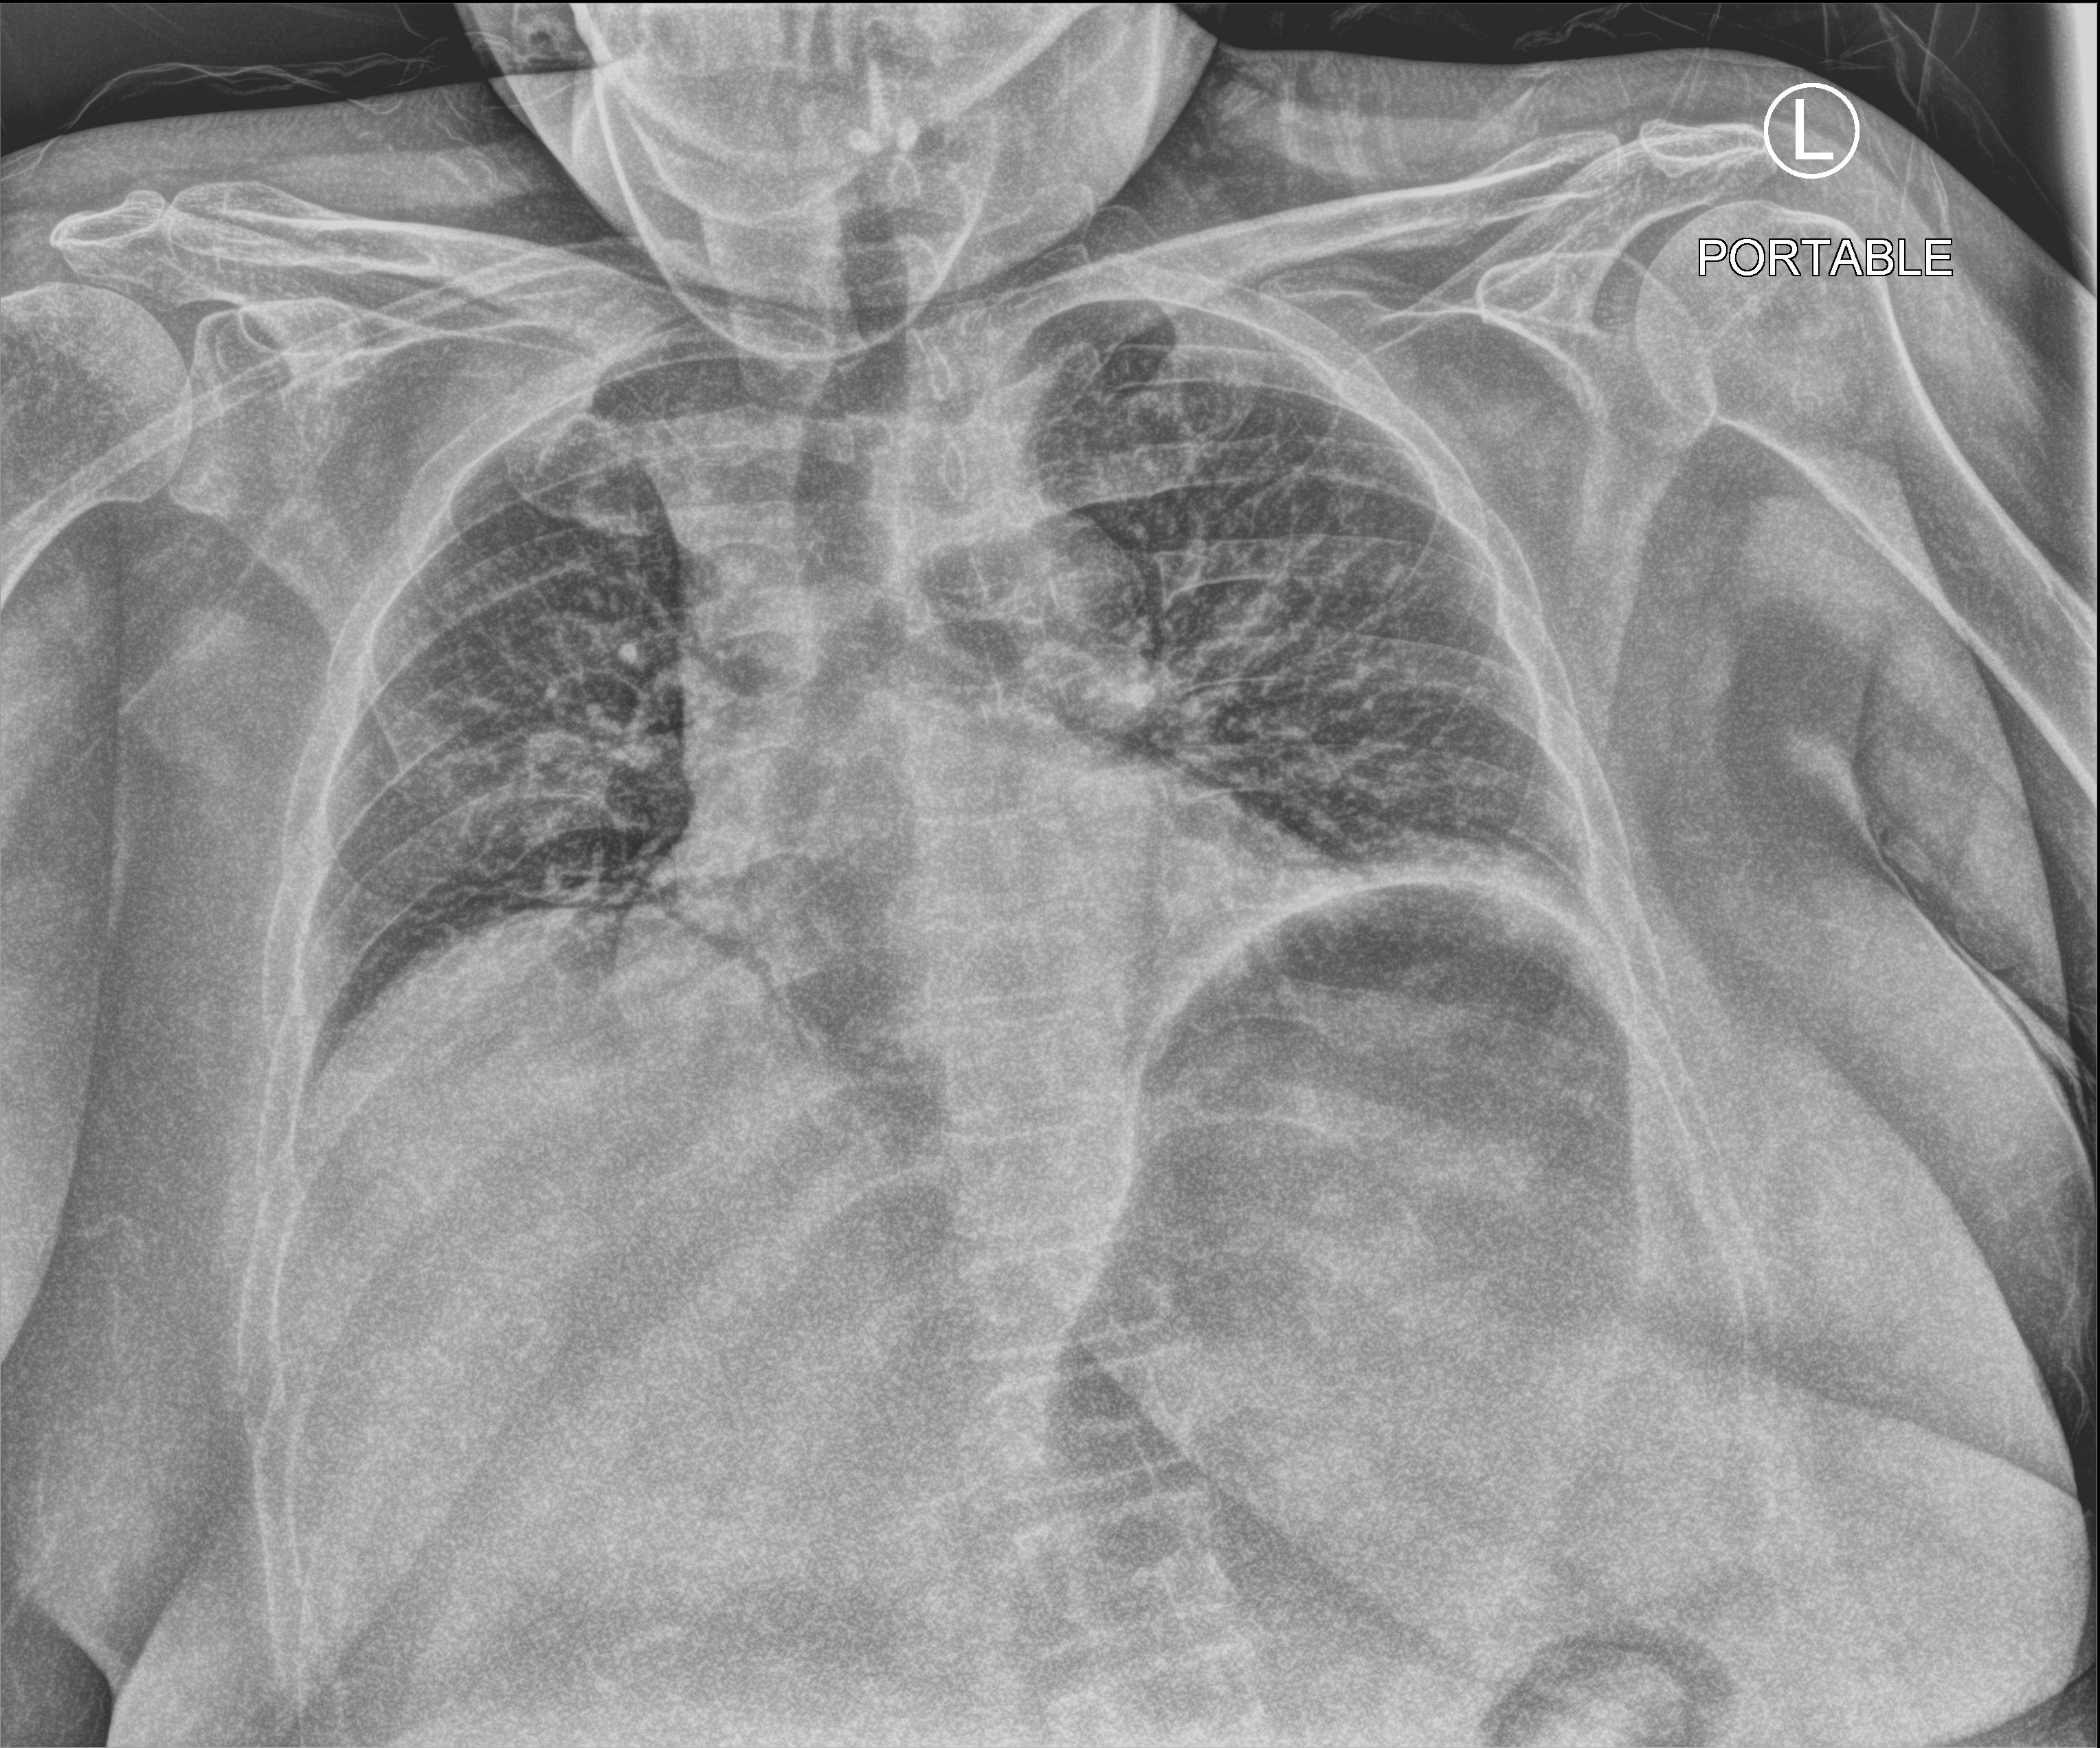
Chest X-ray (portable), anteroposterior (AP) projection. Female patient hospitalised with COVID-19, age 18–59 years.
Hospital-stay facts (about this admission, not read from this image; timing relative to this image not recorded):
- mechanically ventilated during this hospital stay: no